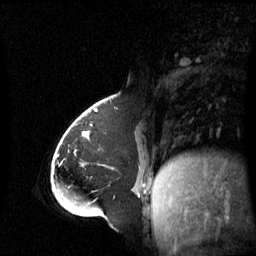
Breast MRI (dynamic contrast-enhanced), one sagittal slice; position 21 of 60 along the scan axis; dynamic contrast-enhanced series, image 2 of 3 at this slice position (ordered by acquisition); 1.5 T; TE 4.2 ms, TR 8.4 ms; 2.8 mm slice thickness; 256 × 256 image matrix, field of view 270 × 270 mm. Female patient, age 43 years. From the clinical record (not read from this slice): setting: breast cancer imaged before/during neoadjuvant chemotherapy; receptor status: triple-negative.
Outlined on this slice (semi-automatic segmentation, software-assisted and operator-edited):
- analysis volume of interest (the breast-tissue region the enhancement analysis was run in; not a lesion): bounding box (x1, y1, x2, y2) in pixels: (65, 118, 143, 198)
- tumour enhancement mask (voxels above the 70 % enhancement threshold inside the analysis volume of interest): (86, 132, 140, 197)